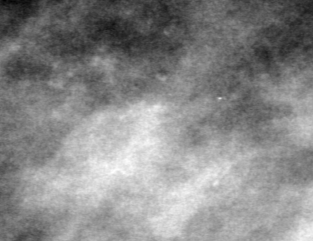
Cropped region of a digitized screen-film mammogram centred on a radiologist-marked abnormality; left breast; MLO view.
Marked abnormality: calcifications, morphology pleomorphic, distribution clustered; BI-RADS assessment category 4; subtlety rating 1 on a 1 (subtle) to 5 (obvious) scale; pathology result (as recorded, not read from the image): benign.